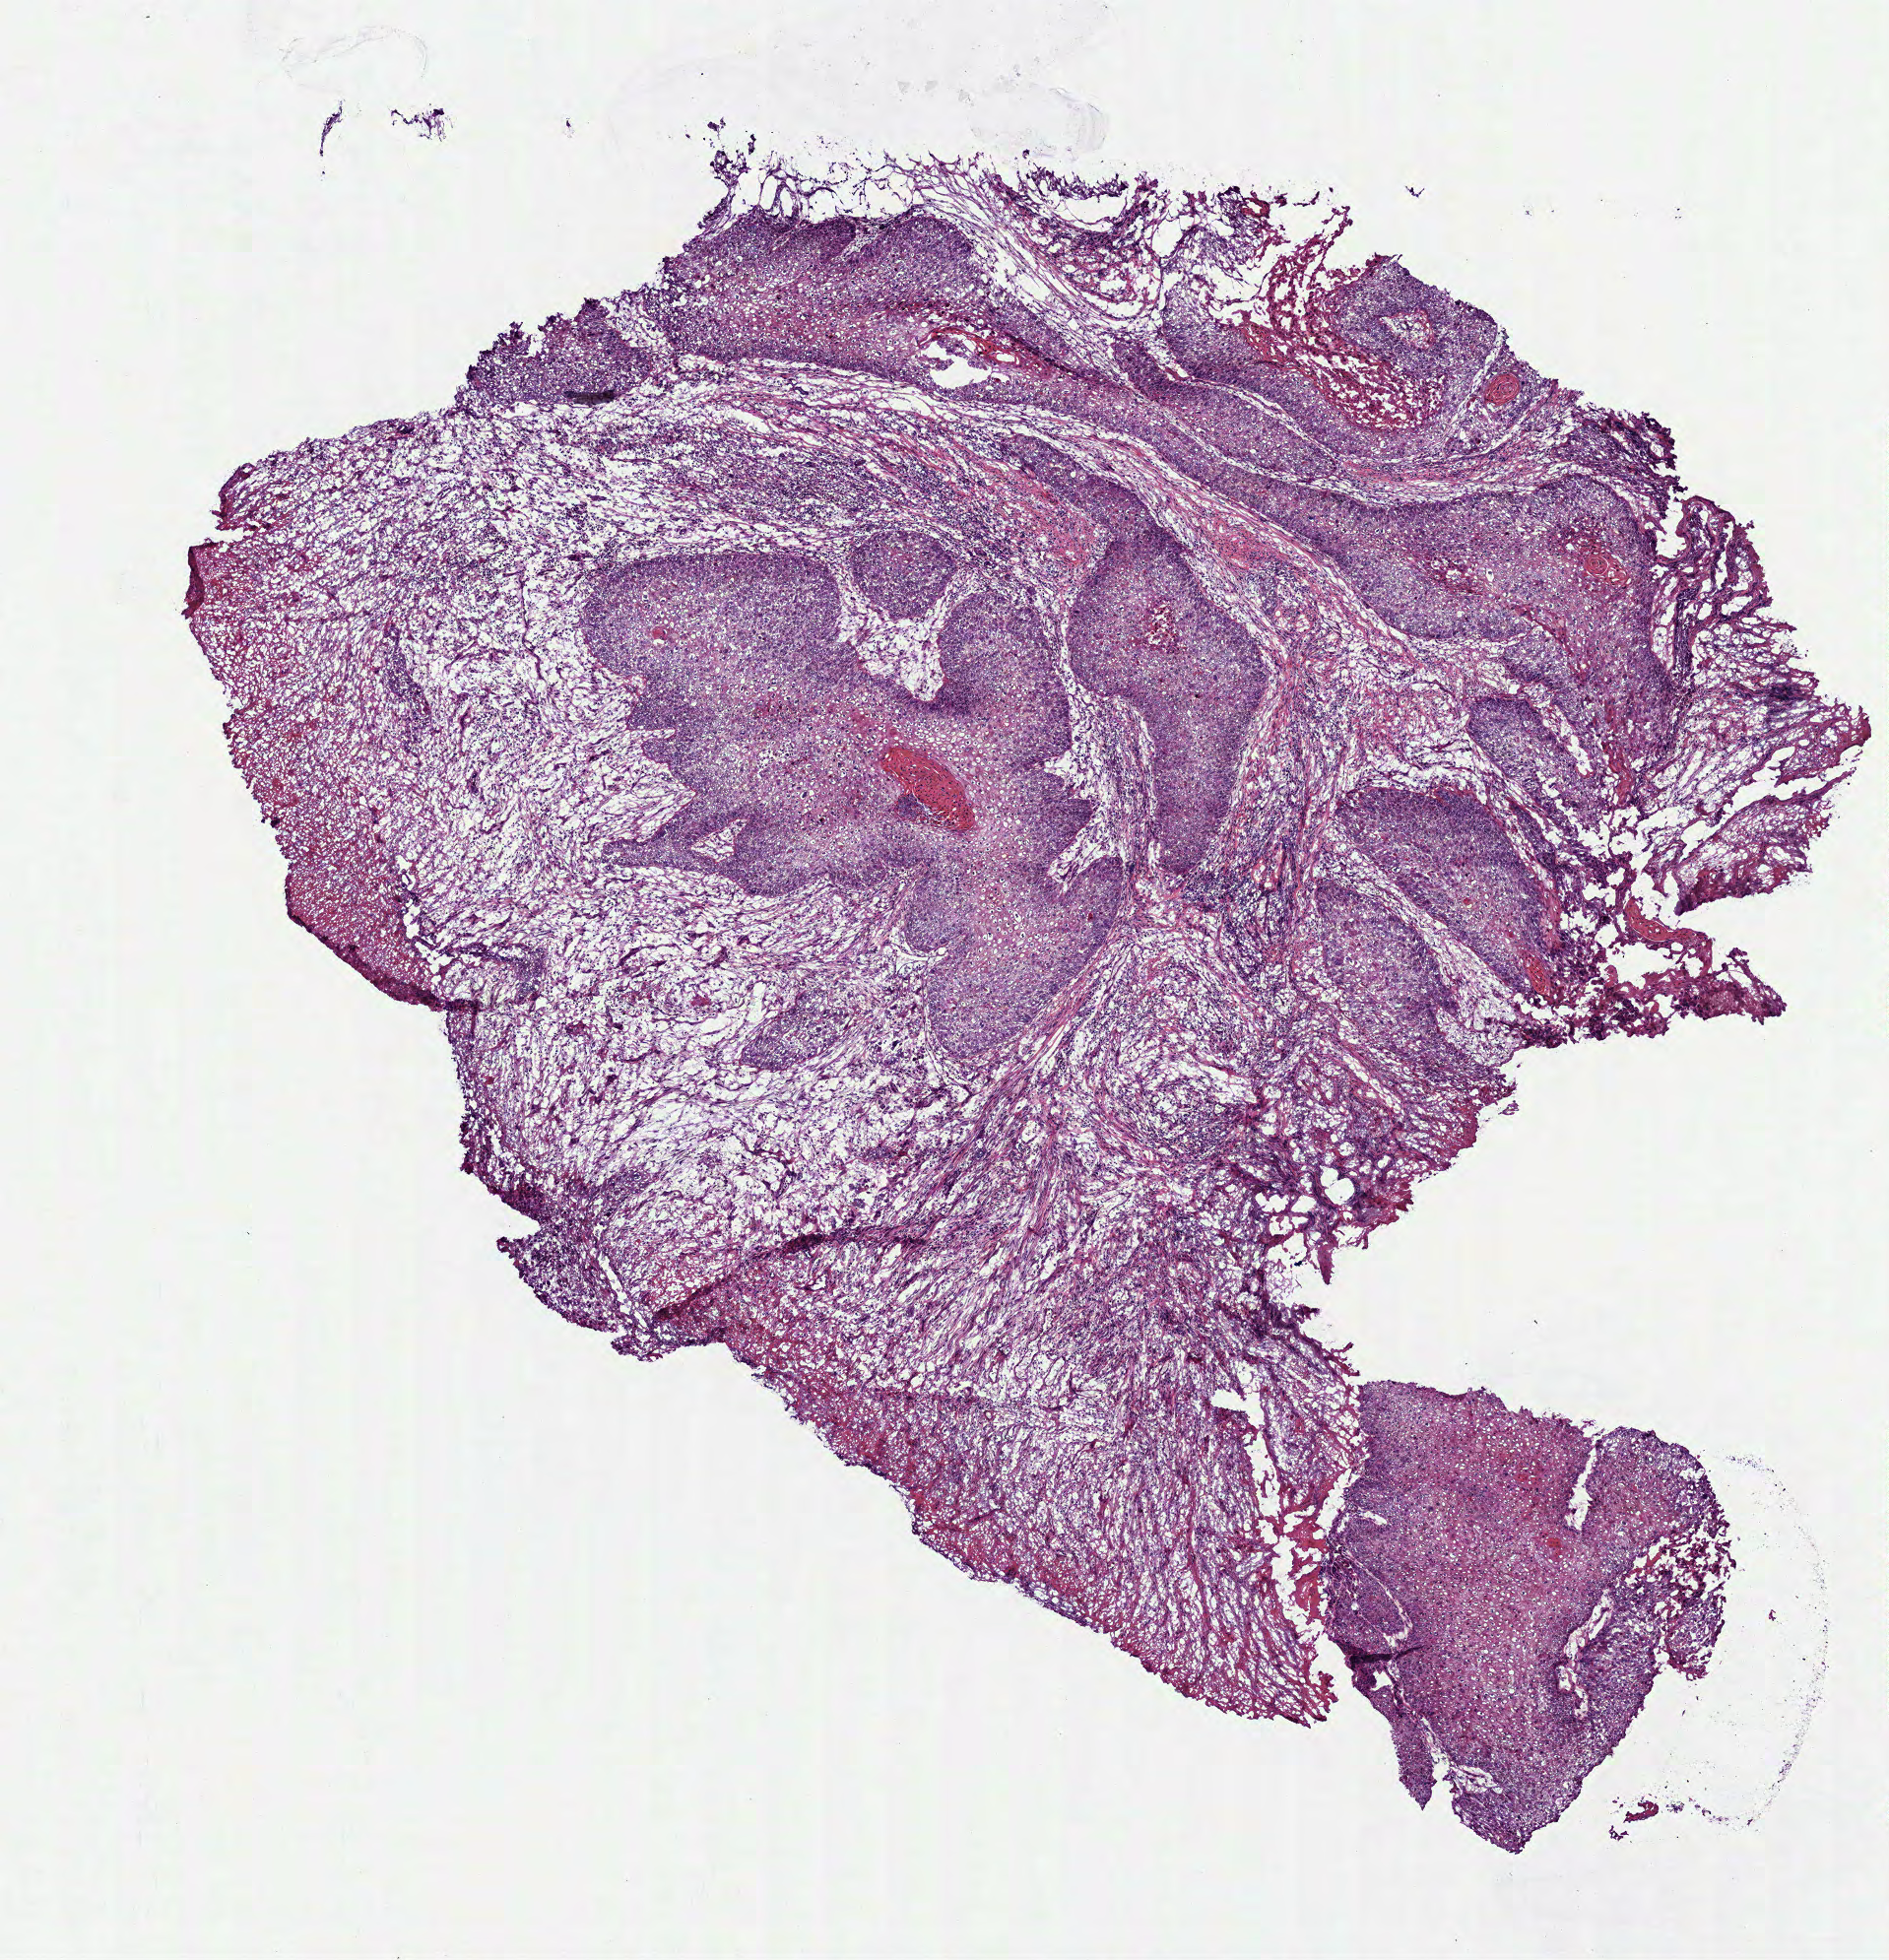
Whole-slide histology image, H&E-stained, whole scanned area (about 7.7 x 8.0 mm, slide scanned at 40x) shown as a low-resolution overview; frozen section; primary tumour sample from the head and neck. Female, age 85 years at initial diagnosis. Pathologist review of this section (percent, as recorded): tumour cells 52%, tumour nuclei 75%.
Pathologic diagnosis: Squamous cell carcinoma, NOS (overlapping lesion of lip, oral cavity and pharynx).